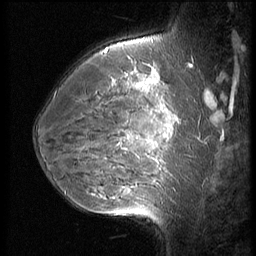
Breast MRI (dynamic contrast-enhanced), one sagittal slice; slice 41 of 56 in the series (ordered by position); 3 images stored at this slice position (order not interpretable as contrast timing); 1.5 T; TE 4.2 ms, TR 9 ms; 2.5 mm slice thickness; 256 × 256 image matrix, field of view 180 × 180 mm. Patient: female, 35 years. From the clinical record (not read from this slice): setting: breast cancer imaged before/during neoadjuvant chemotherapy; receptor status: HR-positive, HER2-negative.
Annotated regions visible in this slice (semi-automatic segmentation, software-assisted and operator-edited):
- analysis volume of interest (the breast-tissue region the enhancement analysis was run in; not a lesion): bounding box [x1, y1, x2, y2] px = [63, 60, 190, 218]
- tumour enhancement mask (voxels above the 140 % enhancement threshold inside the analysis volume of interest): [122, 84, 171, 150]